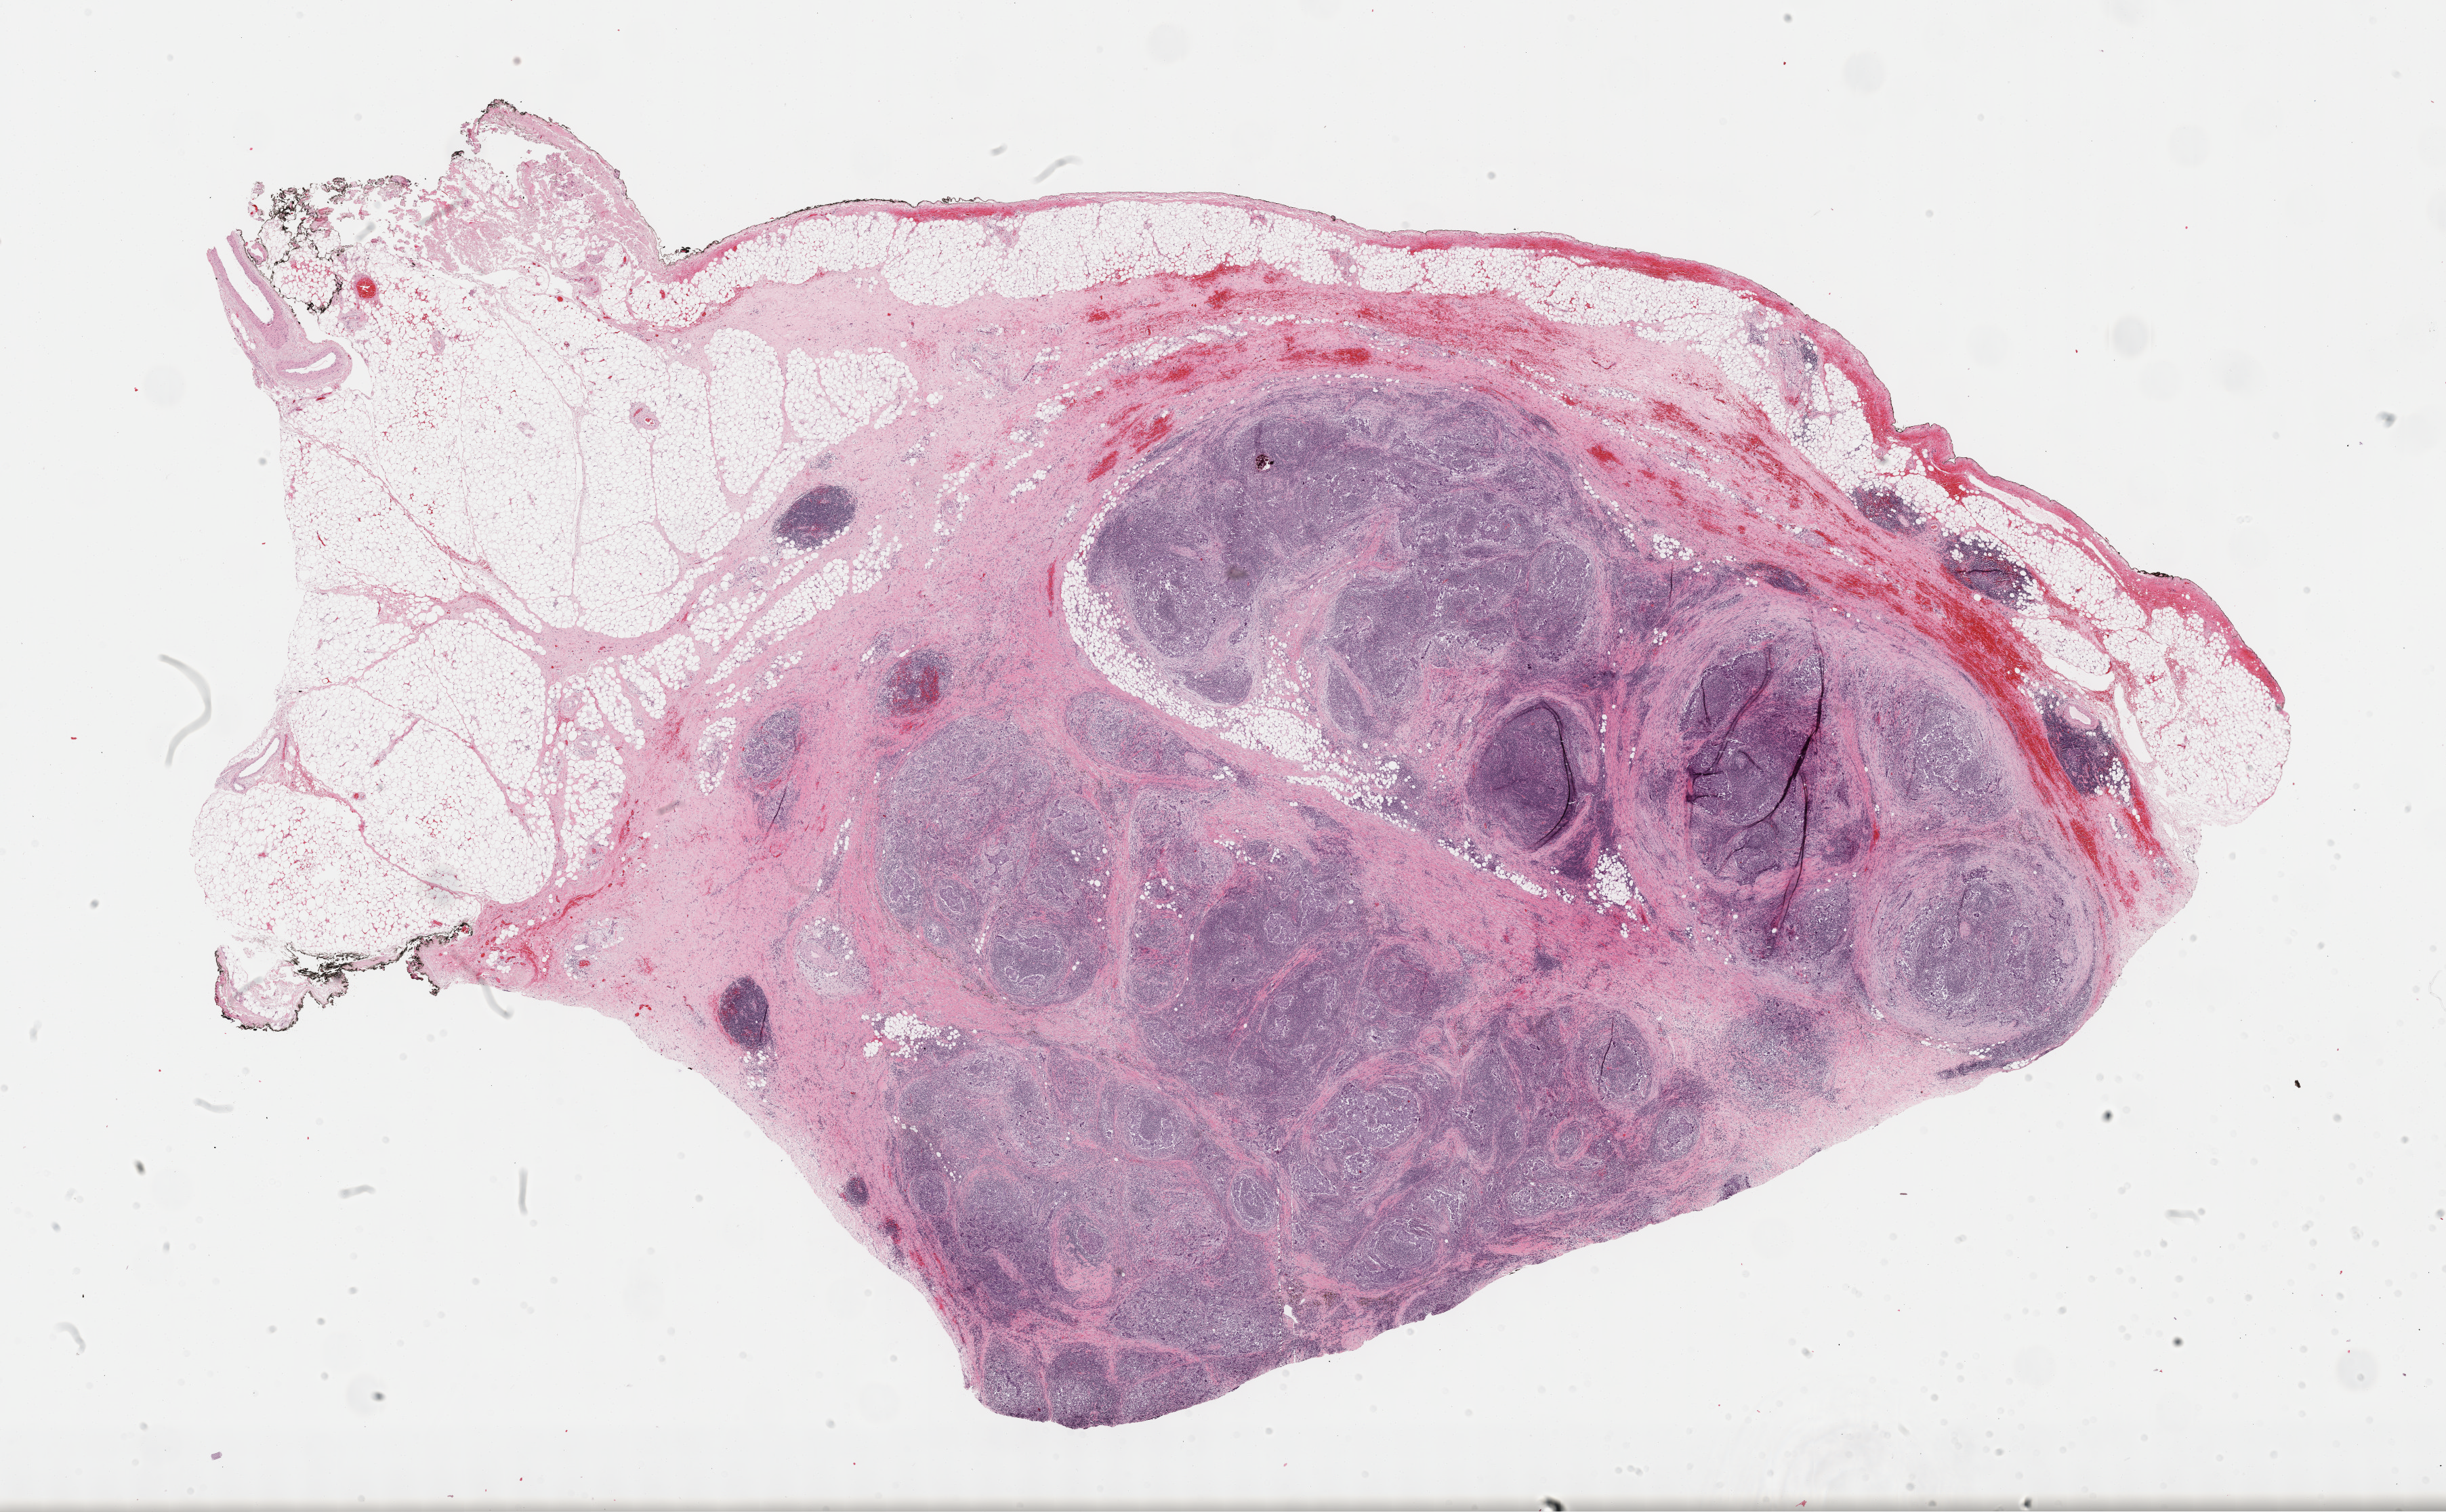
Digitized Hematoxylin and eosin (H&E) stained tissue section (whole slide), low-resolution overview of the scanned area, about 29.2 x 18.1 mm (slide scanned at 40x); formalin-fixed paraffin-embedded (FFPE) diagnostic section; thymus, primary tumour sample. Patient: female, age at initial diagnosis 67 years.
Pathologic diagnosis: Thymic carcinoma, NOS.